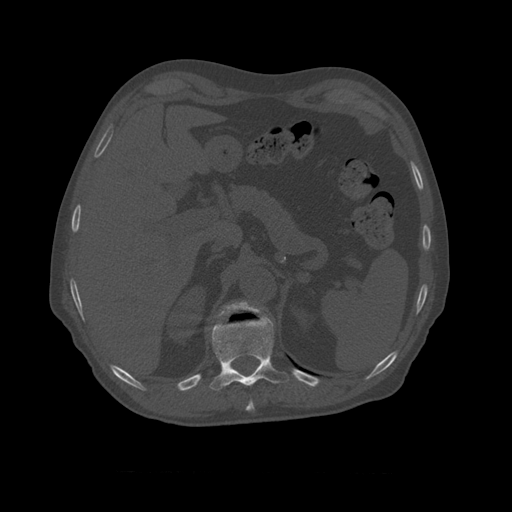
CT including the spine, one axial slice. Slice 400 of 450 in the series (ordered by position). Reconstruction kernel STANDARD. Bone window (W 1800 / L 400 HU). 1.25 mm slice thickness. 512 × 512 image matrix, field of view 405 × 405 mm. Patient age 75 years. Case-level facts recorded for this patient, not image findings: primary cancer: prostate.
Outlined on this slice (semi-automatic segmentation, software-assisted and operator-edited):
- T10 vertebra: bounding box <209,314,290,391> (left, top, right, bottom; pixels)
- T11 vertebra: <217,301,264,321>
- T9 vertebra: <247,400,255,410>